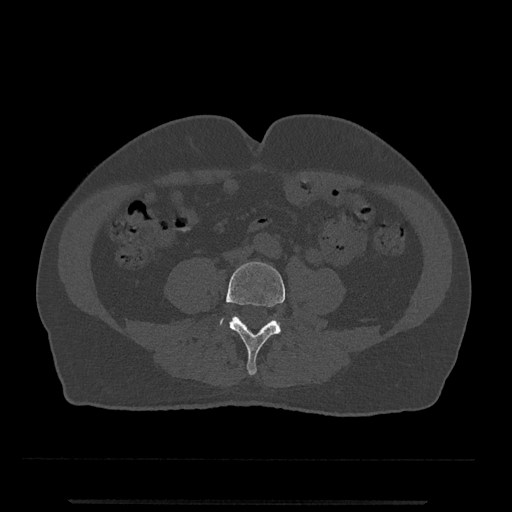
CT including the spine, one axial slice; position 127 of 797 along the scan axis; 120 kVp; bone window (W 1800 / L 400 HU); 0.5 mm slice thickness; 512 × 512 image matrix, field of view 419 × 419 mm. Male patient, age 63 years. Case-level facts recorded for this patient, not image findings: primary cancer: prostate.
Outlined on this slice (semi-automatic segmentation, software-assisted and operator-edited):
- L4 vertebra: bounding box (x1, y1, x2, y2) in pixels: (226, 261, 285, 375)
- L5 vertebra: (220, 319, 280, 327)